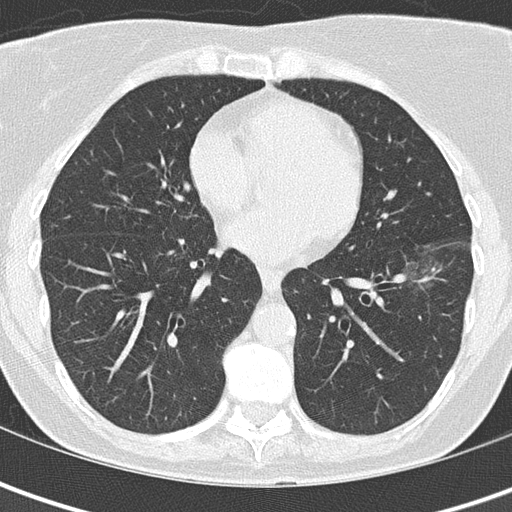
Axial slice from a low-dose chest CT screening exam; baseline screening round; lung window (W 1500 / L -600 HU); 120 kVp; slice 87 of 149 in the series; 512 × 512 image matrix, field of view 280 × 280 mm. Female, age 61 years at enrolment. Former smoker at enrolment.
Expert-annotated lung lesion, box from (x=381, y=247) to (x=457, y=307) px. Screening reader's record for this exam (one nodule recorded; not confirmed to be the boxed lesion): non-calcified nodule or mass ≥4 mm, left lower lobe, 29 × 16 mm, ground glass attenuation. Participant outcome: lung cancer diagnosed 259 days after this screen — bronchiolo-alveolar adenocarcinoma, NOS, left lower lobe, well differentiated (G1), stage IA (AJCC 6th edition), 10 mm at pathology.